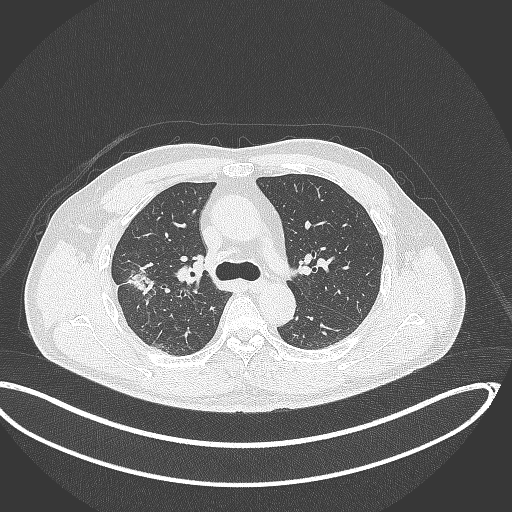
Chest CT, one axial slice; slice 226 of 391 in the series (ordered by position); reconstruction kernel B70f; 120 kVp; lung window (W 1500 / L -600 HU); 1 mm slice thickness; 512 × 512 image matrix. Male patient, age 63 years. Case-level facts recorded for this patient, not image findings: clinical TNM (as recorded): T1c N0 M0; histopathological grade: G2-3.
Annotated regions visible in this slice (bounding box drawn by a radiologist):
- lung tumour (recorded histology: adenocarcinoma): bounding box (x1, y1, x2, y2) in pixels: (119, 259, 162, 300)